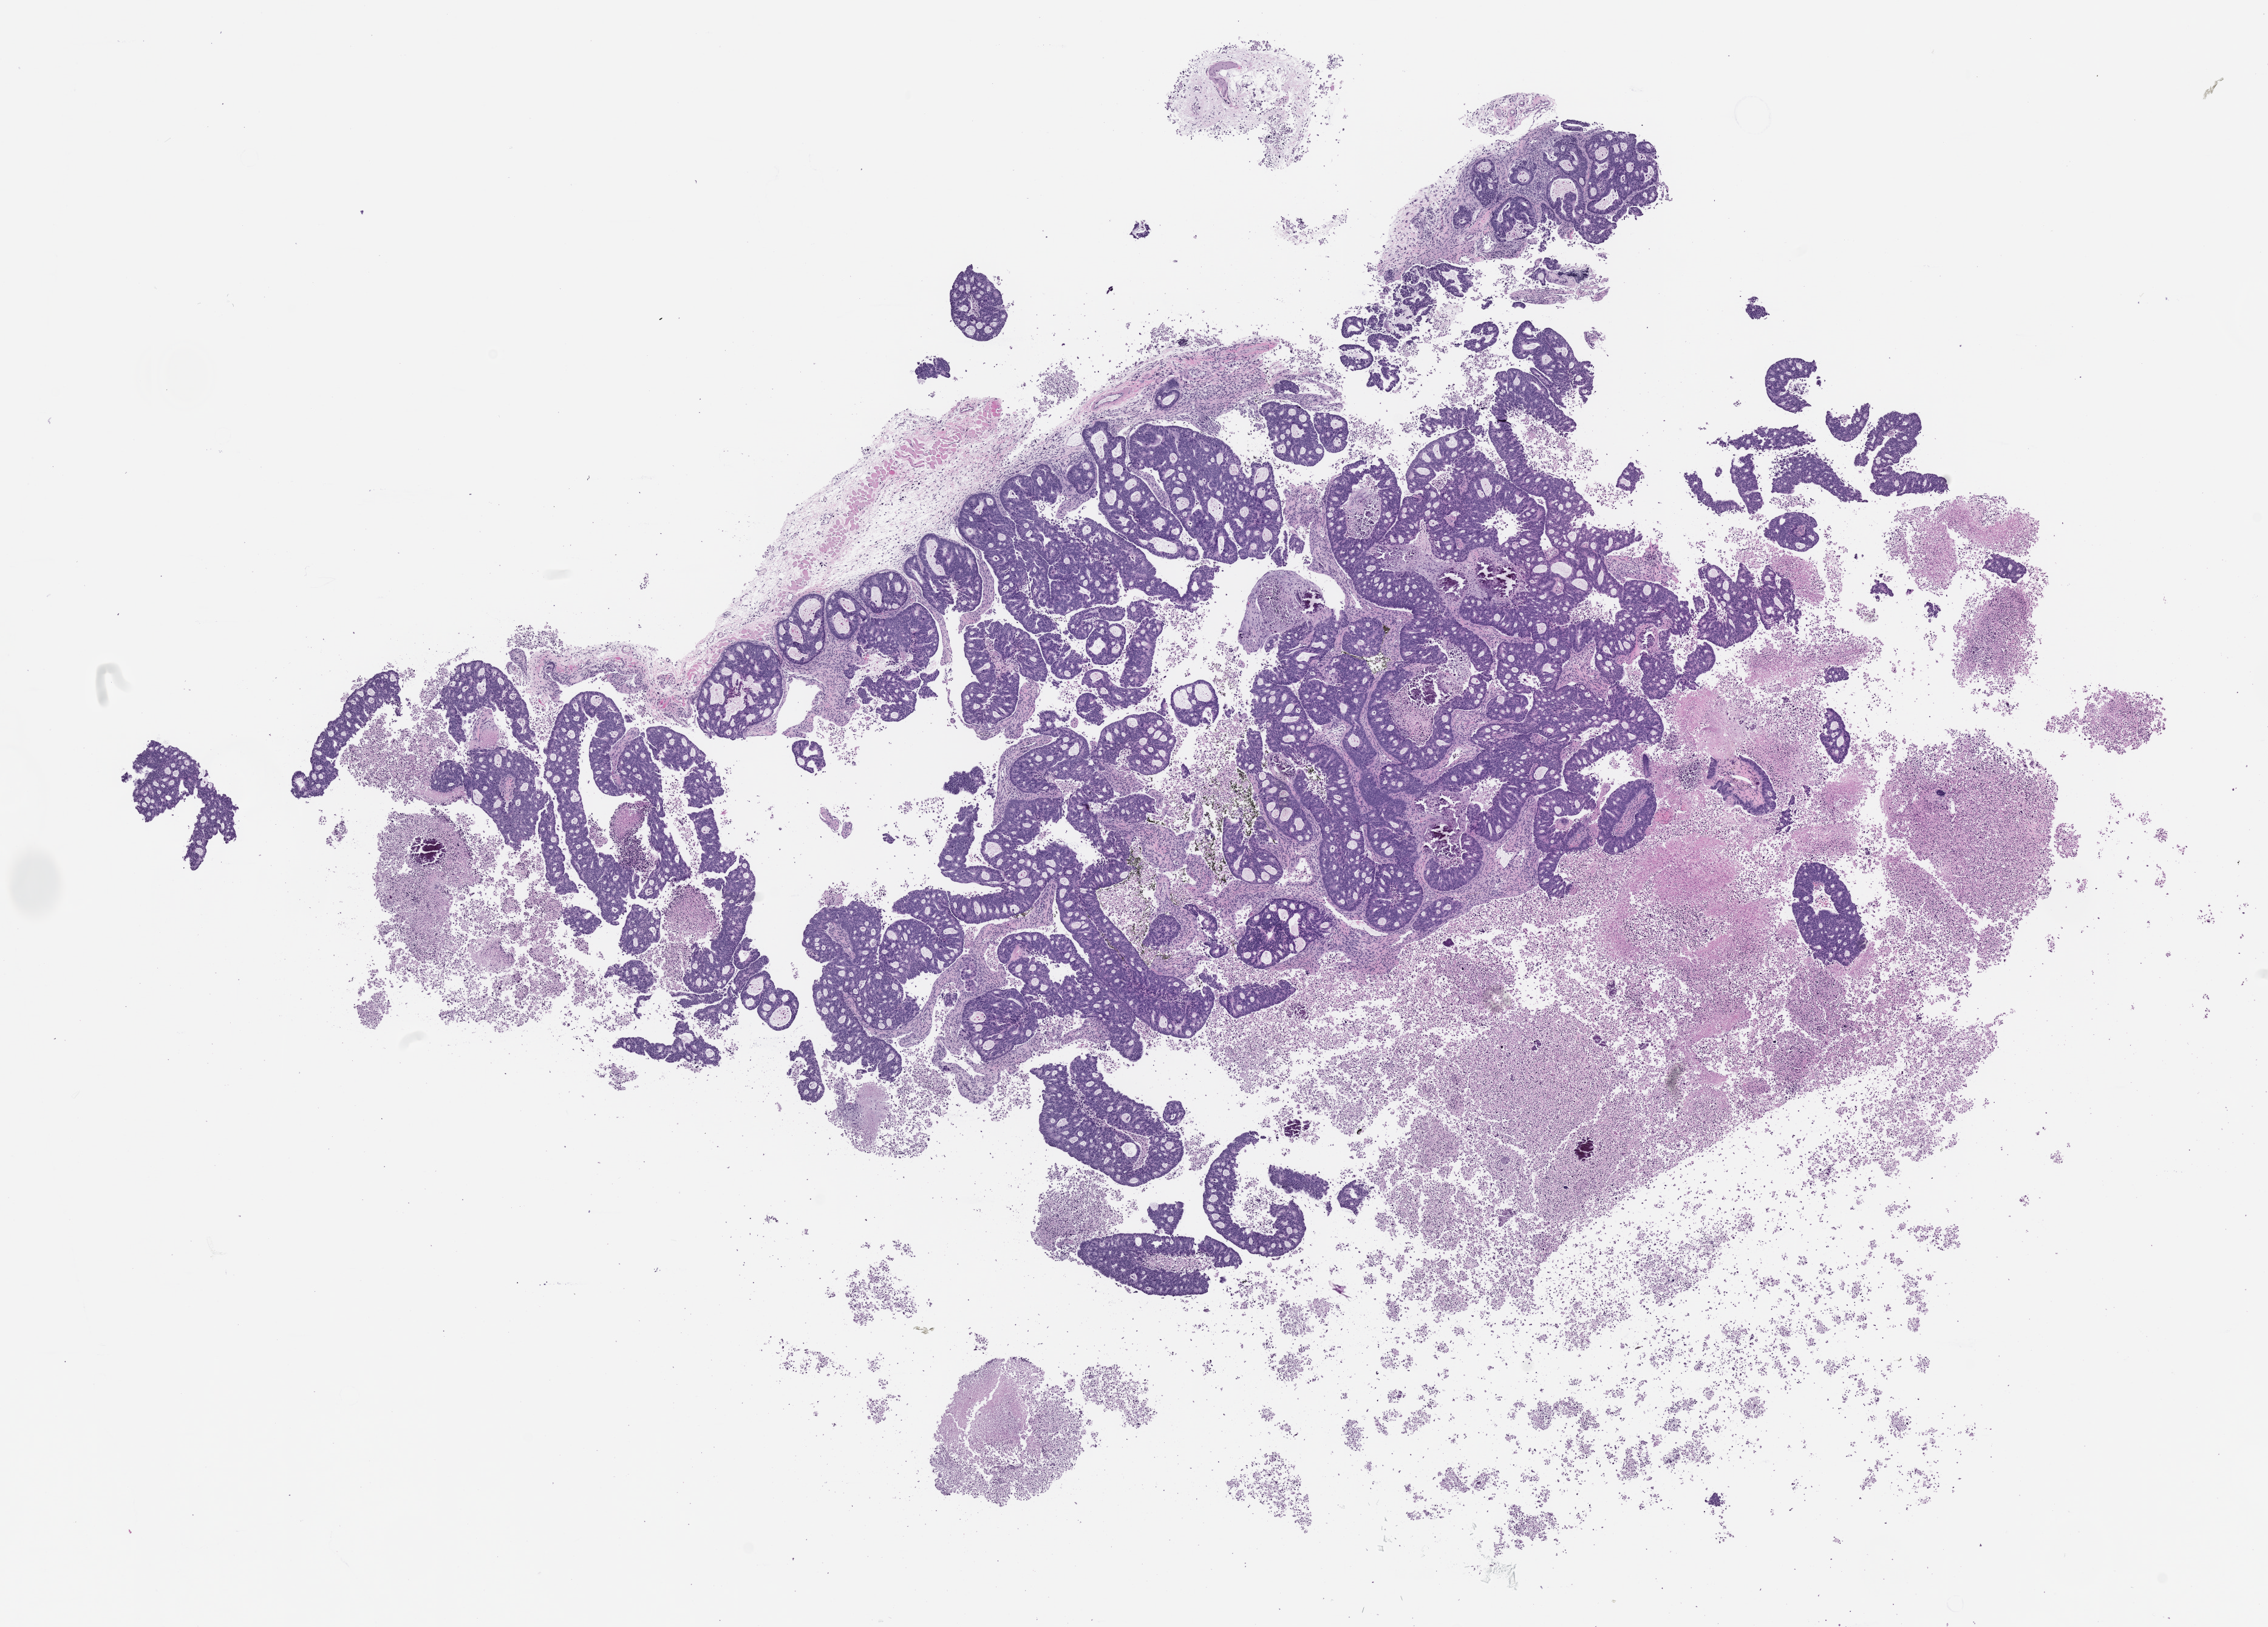
H&E whole-slide image of a patient-derived xenograft (PDX) tumor grown in a mouse, passage 1 — low-resolution overview of the scanned area, about 15.0 x 10.8 mm, FFPE section, tumor site category: rectum.
Originating patient diagnosis: Rectal Adenocarcinoma.